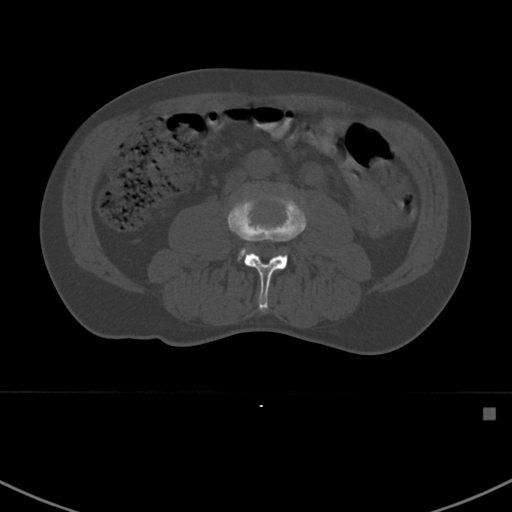
CT including the spine, one axial slice; slice 258 of 412 in the series (ordered by position); reconstruction kernel Br40s; 120 kVp; bone window (W 1800 / L 400 HU); 512 × 512 image matrix. Male patient, age 59 years. Case-level facts recorded for this patient, not image findings: primary cancer: prostate.
Outlined on this slice (semi-automatically segmented with operator editing):
- L3 vertebra: bounding box [x1, y1, x2, y2] px = [228, 194, 307, 312]
- L4 vertebra: [238, 247, 249, 259]